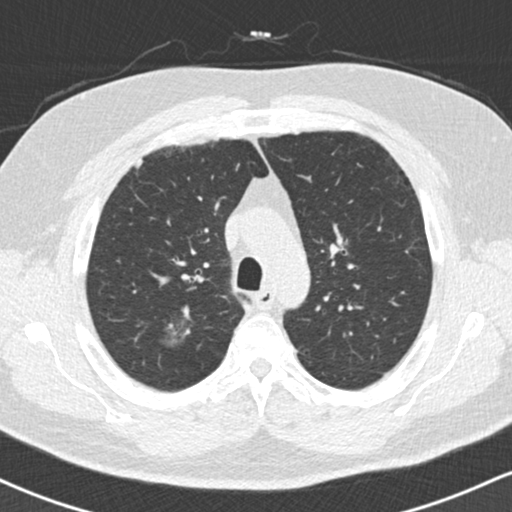
Axial slice from a low-dose chest CT screening exam; second annual screen; lung window (W 1500 / L -600 HU); 2 mm slice thickness; standard (soft-tissue) reconstruction kernel (B30f); 120 kVp; slice 47 of 169 in the series; 512 × 512 image matrix, field of view 320 × 320 mm. Male, age 59 years at enrolment. Current smoker at enrolment.
• Expert reader's lesion annotation, box from (x=153, y=302) to (x=209, y=360) px.
• Reader record for this screening exam (exam-level; its link to the box is not recorded): non-calcified nodule or mass ≥4 mm, right upper lobe, 18 × 16 mm, ground glass attenuation, pre-existing on the prior screen: yes.
• Official screen result: positive, no significant change: stable abnormalities potentially related to lung cancer, unchanged since the prior screening exam.
• Lung cancer was diagnosed 60 days after this screen: bronchiolo-alveolar adenocarcinoma, NOS, right lower lobe, stage IA (AJCC 6th edition), 15 mm at pathology.